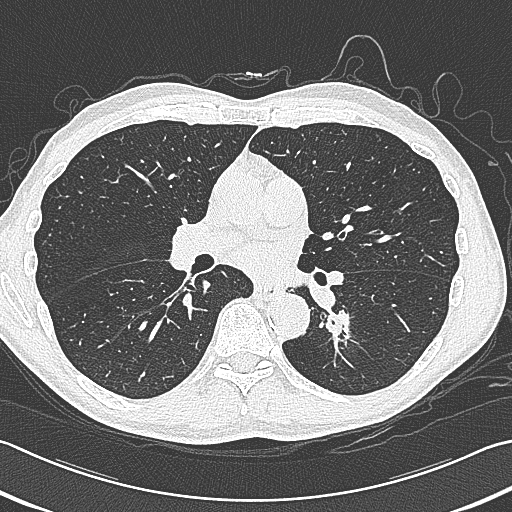
Chest CT (low-dose screening protocol), one axial image. Baseline annual screen. Lung window (W 1500 / L -600 HU). Lung (sharp) reconstruction kernel (B80f). Male, age 59 years at enrolment. Former smoker at enrolment.
• Expert-annotated lung lesion, bounding box <313,293,375,352> (left, top, right, bottom; pixels).
• Screening reader's record for this exam (one nodule recorded; not confirmed to be the boxed lesion): non-calcified nodule or mass ≥4 mm, left lower lobe, 15 × 15 mm, smooth margins, soft tissue attenuation.
• Participant outcome: lung cancer diagnosed 17 days after this screen — squamous cell carcinoma, large cell, nonkeratinizing, NOS, left lower lobe, poorly differentiated (G3), stage IB (AJCC 6th edition), 31 mm at pathology.